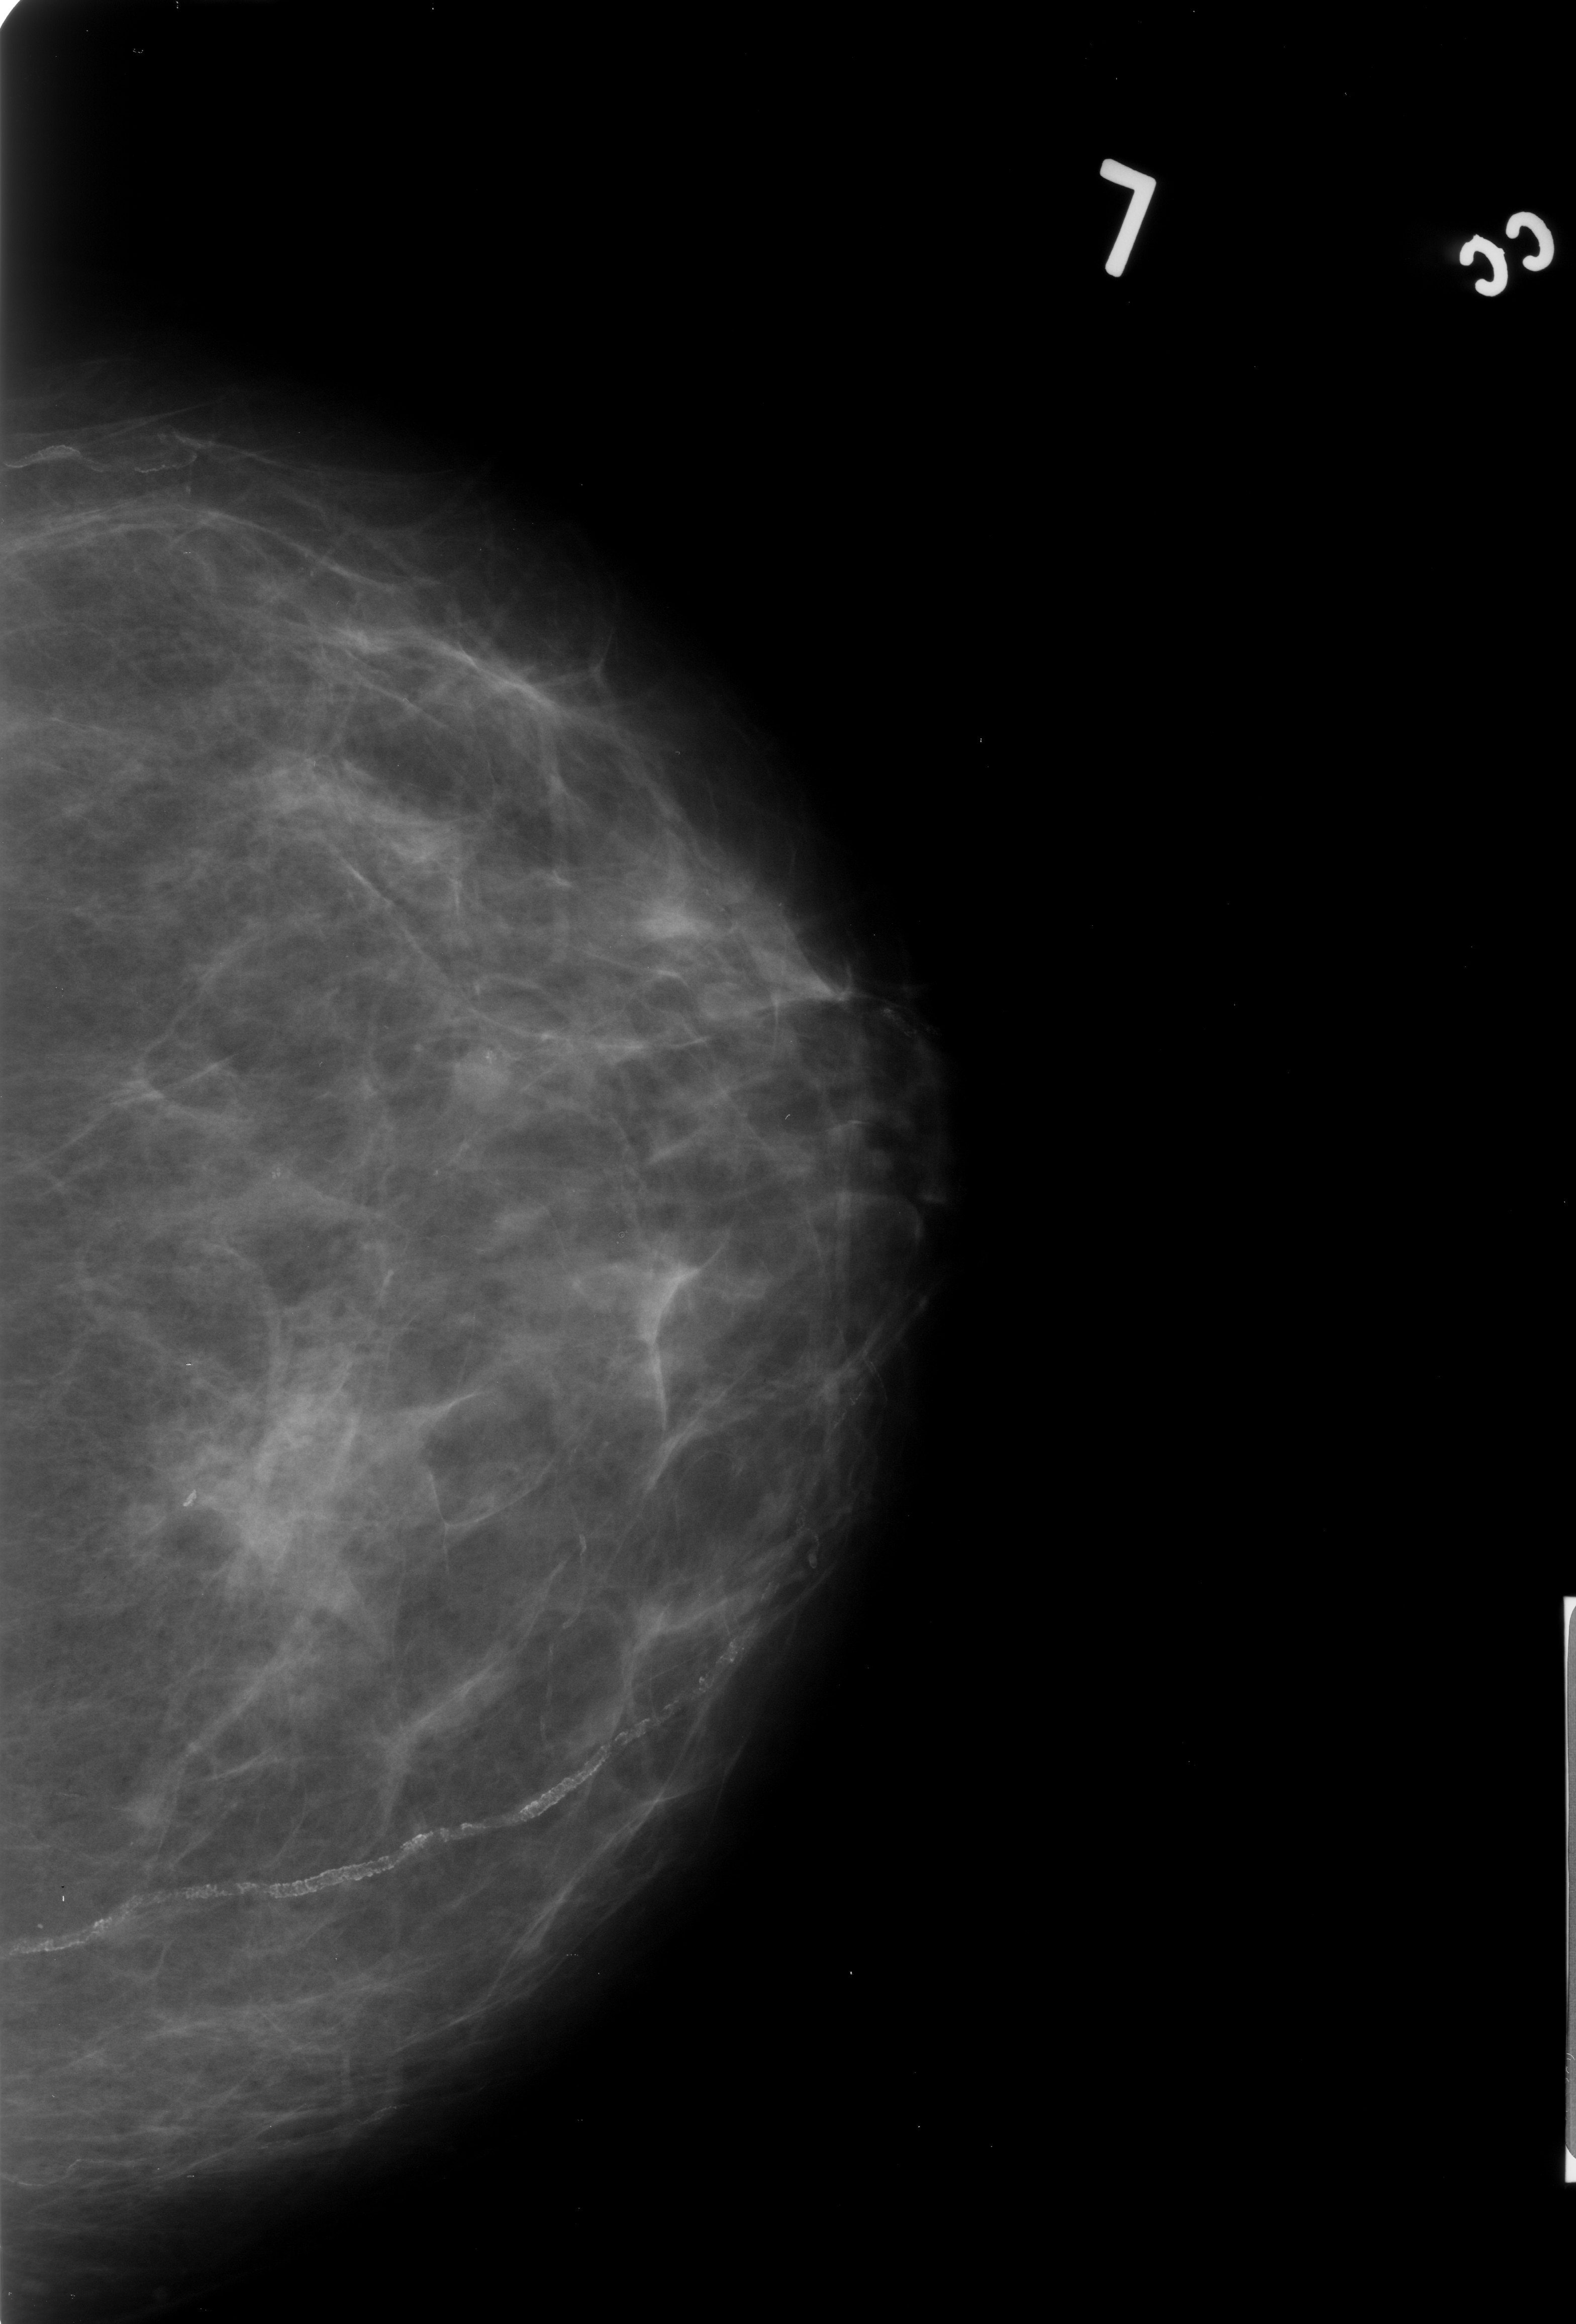
Mammogram (digitized film); left breast; CC view; breast composition: scattered fibroglandular densities (BI-RADS density category 2 of 4).
Radiologist-marked abnormalities on this image: Finding 1 of 2: calcifications, morphology pleomorphic, distribution clustered; BI-RADS assessment category 4; pathology (as recorded): benign. Finding 2 of 2: calcifications, morphology pleomorphic, distribution clustered; BI-RADS assessment category 4; subtlety rating 2 on a 1 (subtle) to 5 (obvious) scale; pathology (as recorded): benign.